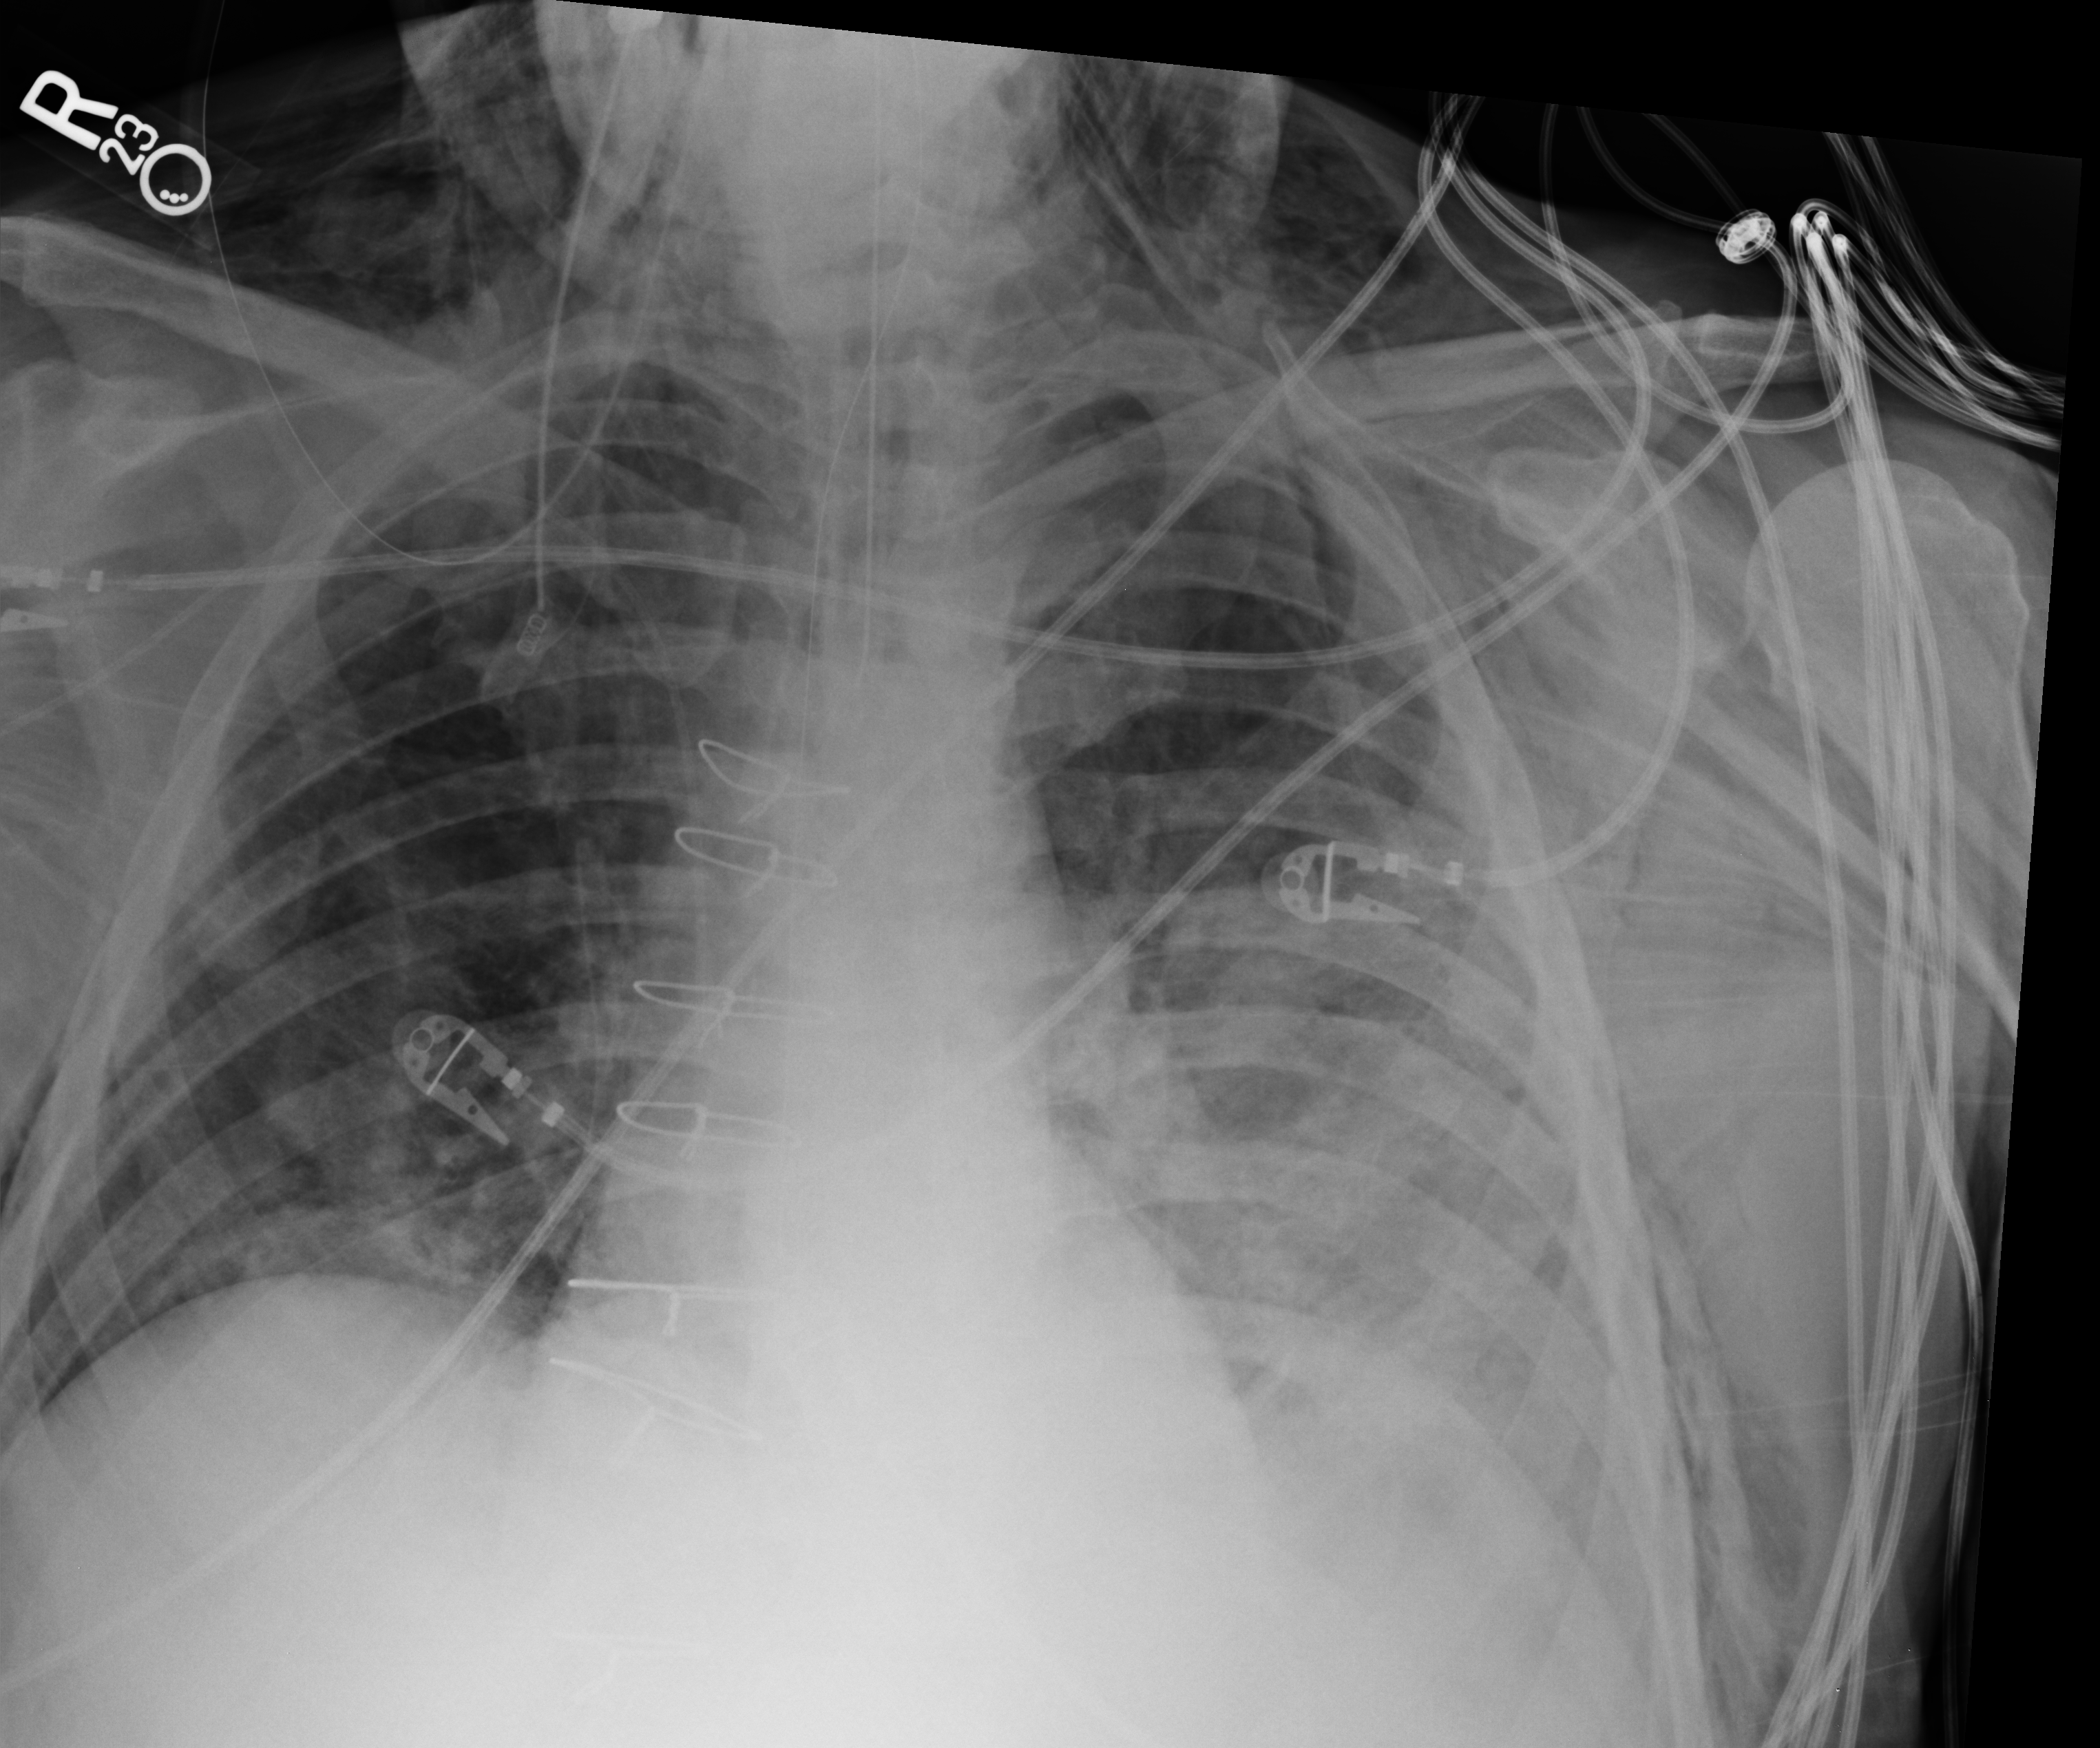
Portable chest radiograph. Male patient hospitalised with COVID-19, age 60–74 years.
From the hospital-stay record, not from the radiograph (when in the stay this image was taken is not recorded):
- mechanically ventilated during this hospital stay: yes
- chronic kidney disease (admission record): no
- hypertension (admission record): yes